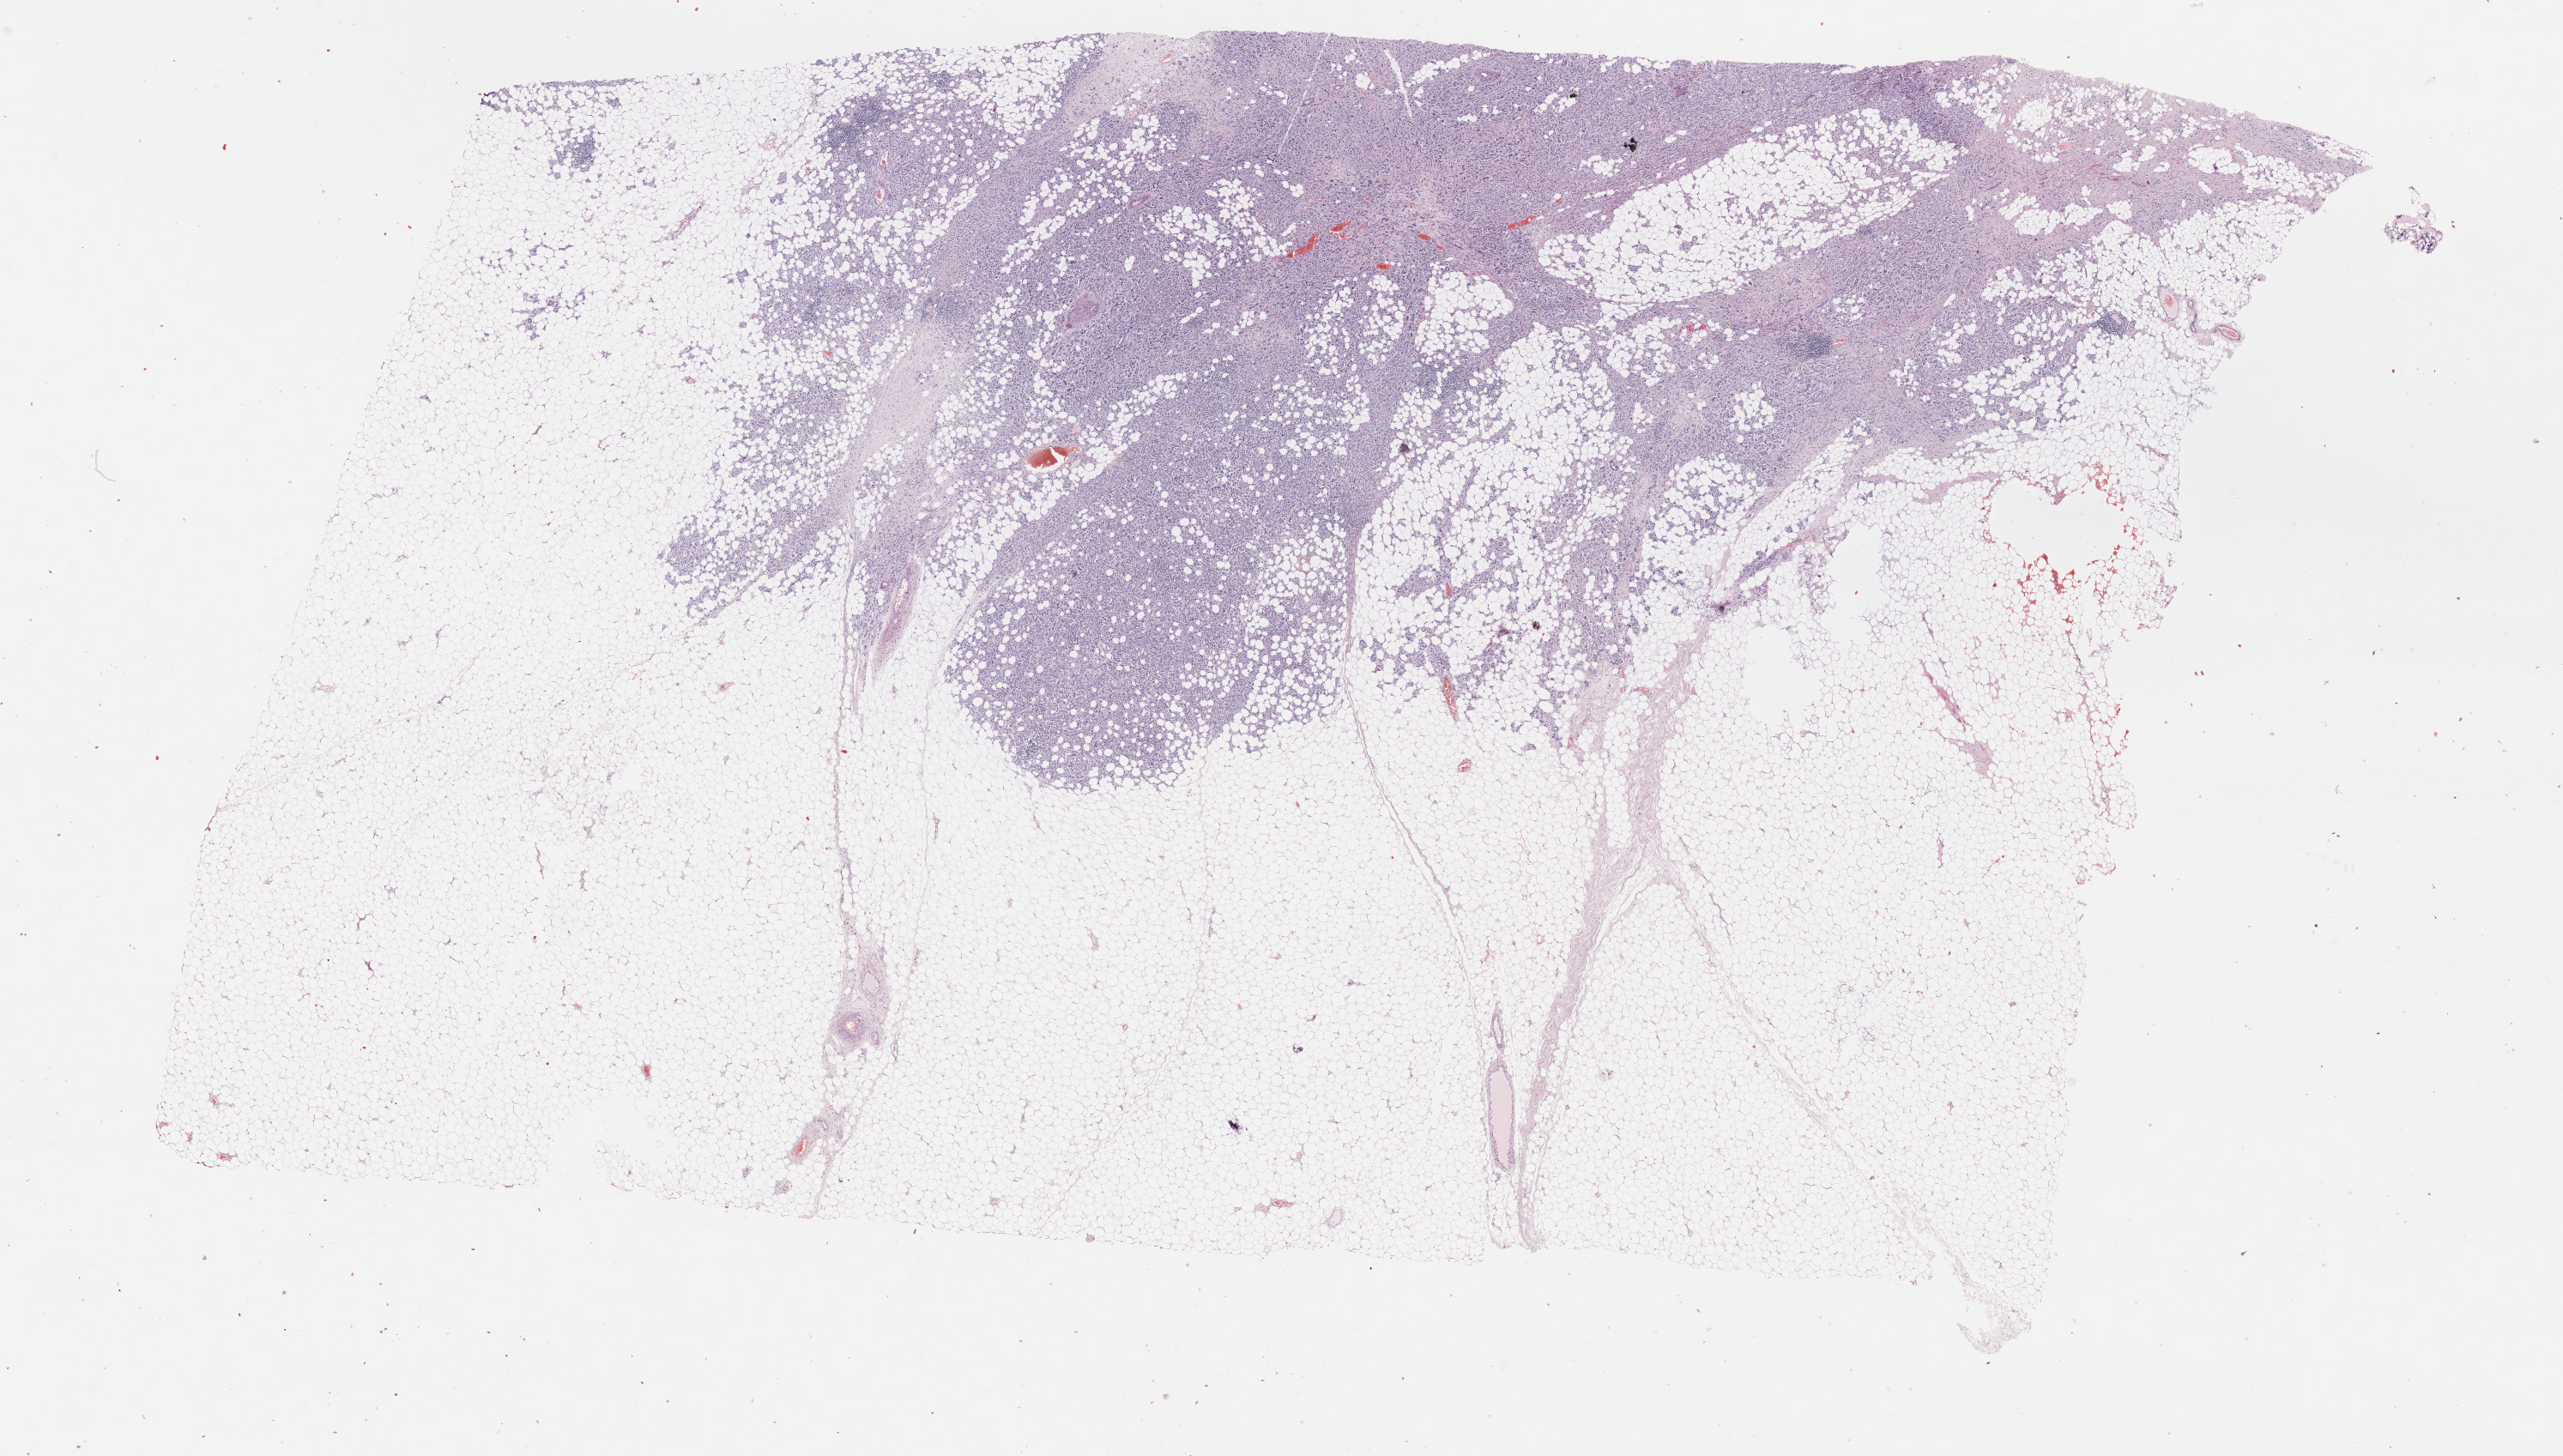
Digitized Hematoxylin and eosin (H&E) stained tissue section (whole slide), whole scanned area (about 24.2 x 13.7 mm, acquisition: 40x scan) shown as a low-resolution overview. FFPE section. Sample: primary tumour, breast. Female patient; age at initial diagnosis 80 years.
Diagnosis: Infiltrating duct carcinoma, NOS. Laterality: right. AJCC pathologic stage: IIA (7th edition).